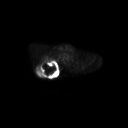
FDG PET of an extremity soft-tissue mass (from a PET/CT study), one axial slice; position 211 of 267 along the scan axis; 3.27 mm slice thickness; 128 × 128 image matrix, field of view 700 × 700 mm. Patient: male, 61 years. Case-level facts recorded for this patient, not image findings: histological type: pleiomorphic spindle cell undifferentiated; grade: high; site of the primary tumour: right parascapusular.
Structures marked on this image (expert contour drawn on MRI and transferred to this co-registered scan by the dataset authors):
- gross tumour volume including surrounding oedema: bounding box [x1, y1, x2, y2] px = [35, 59, 61, 77]
- gross tumour volume (mass): [36, 60, 57, 76]